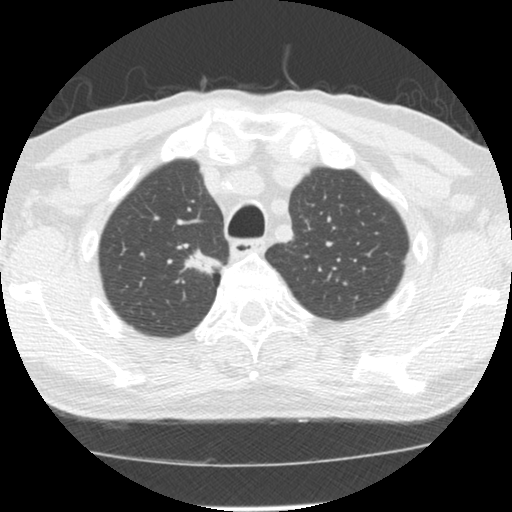
Low-dose screening chest CT, one axial slice. Position 110 of 139 along the scan axis. Reconstruction kernel STANDARD. Lung window (W 1500 / L -600 HU). 2.5 mm slice thickness. 512 × 512 image matrix, field of view 310 × 310 mm.
Outlined on this slice (outlined manually by an expert reader):
- lesion 1 (tumor, upper lobe of right lung): box from (x=181, y=249) to (x=223, y=276) px